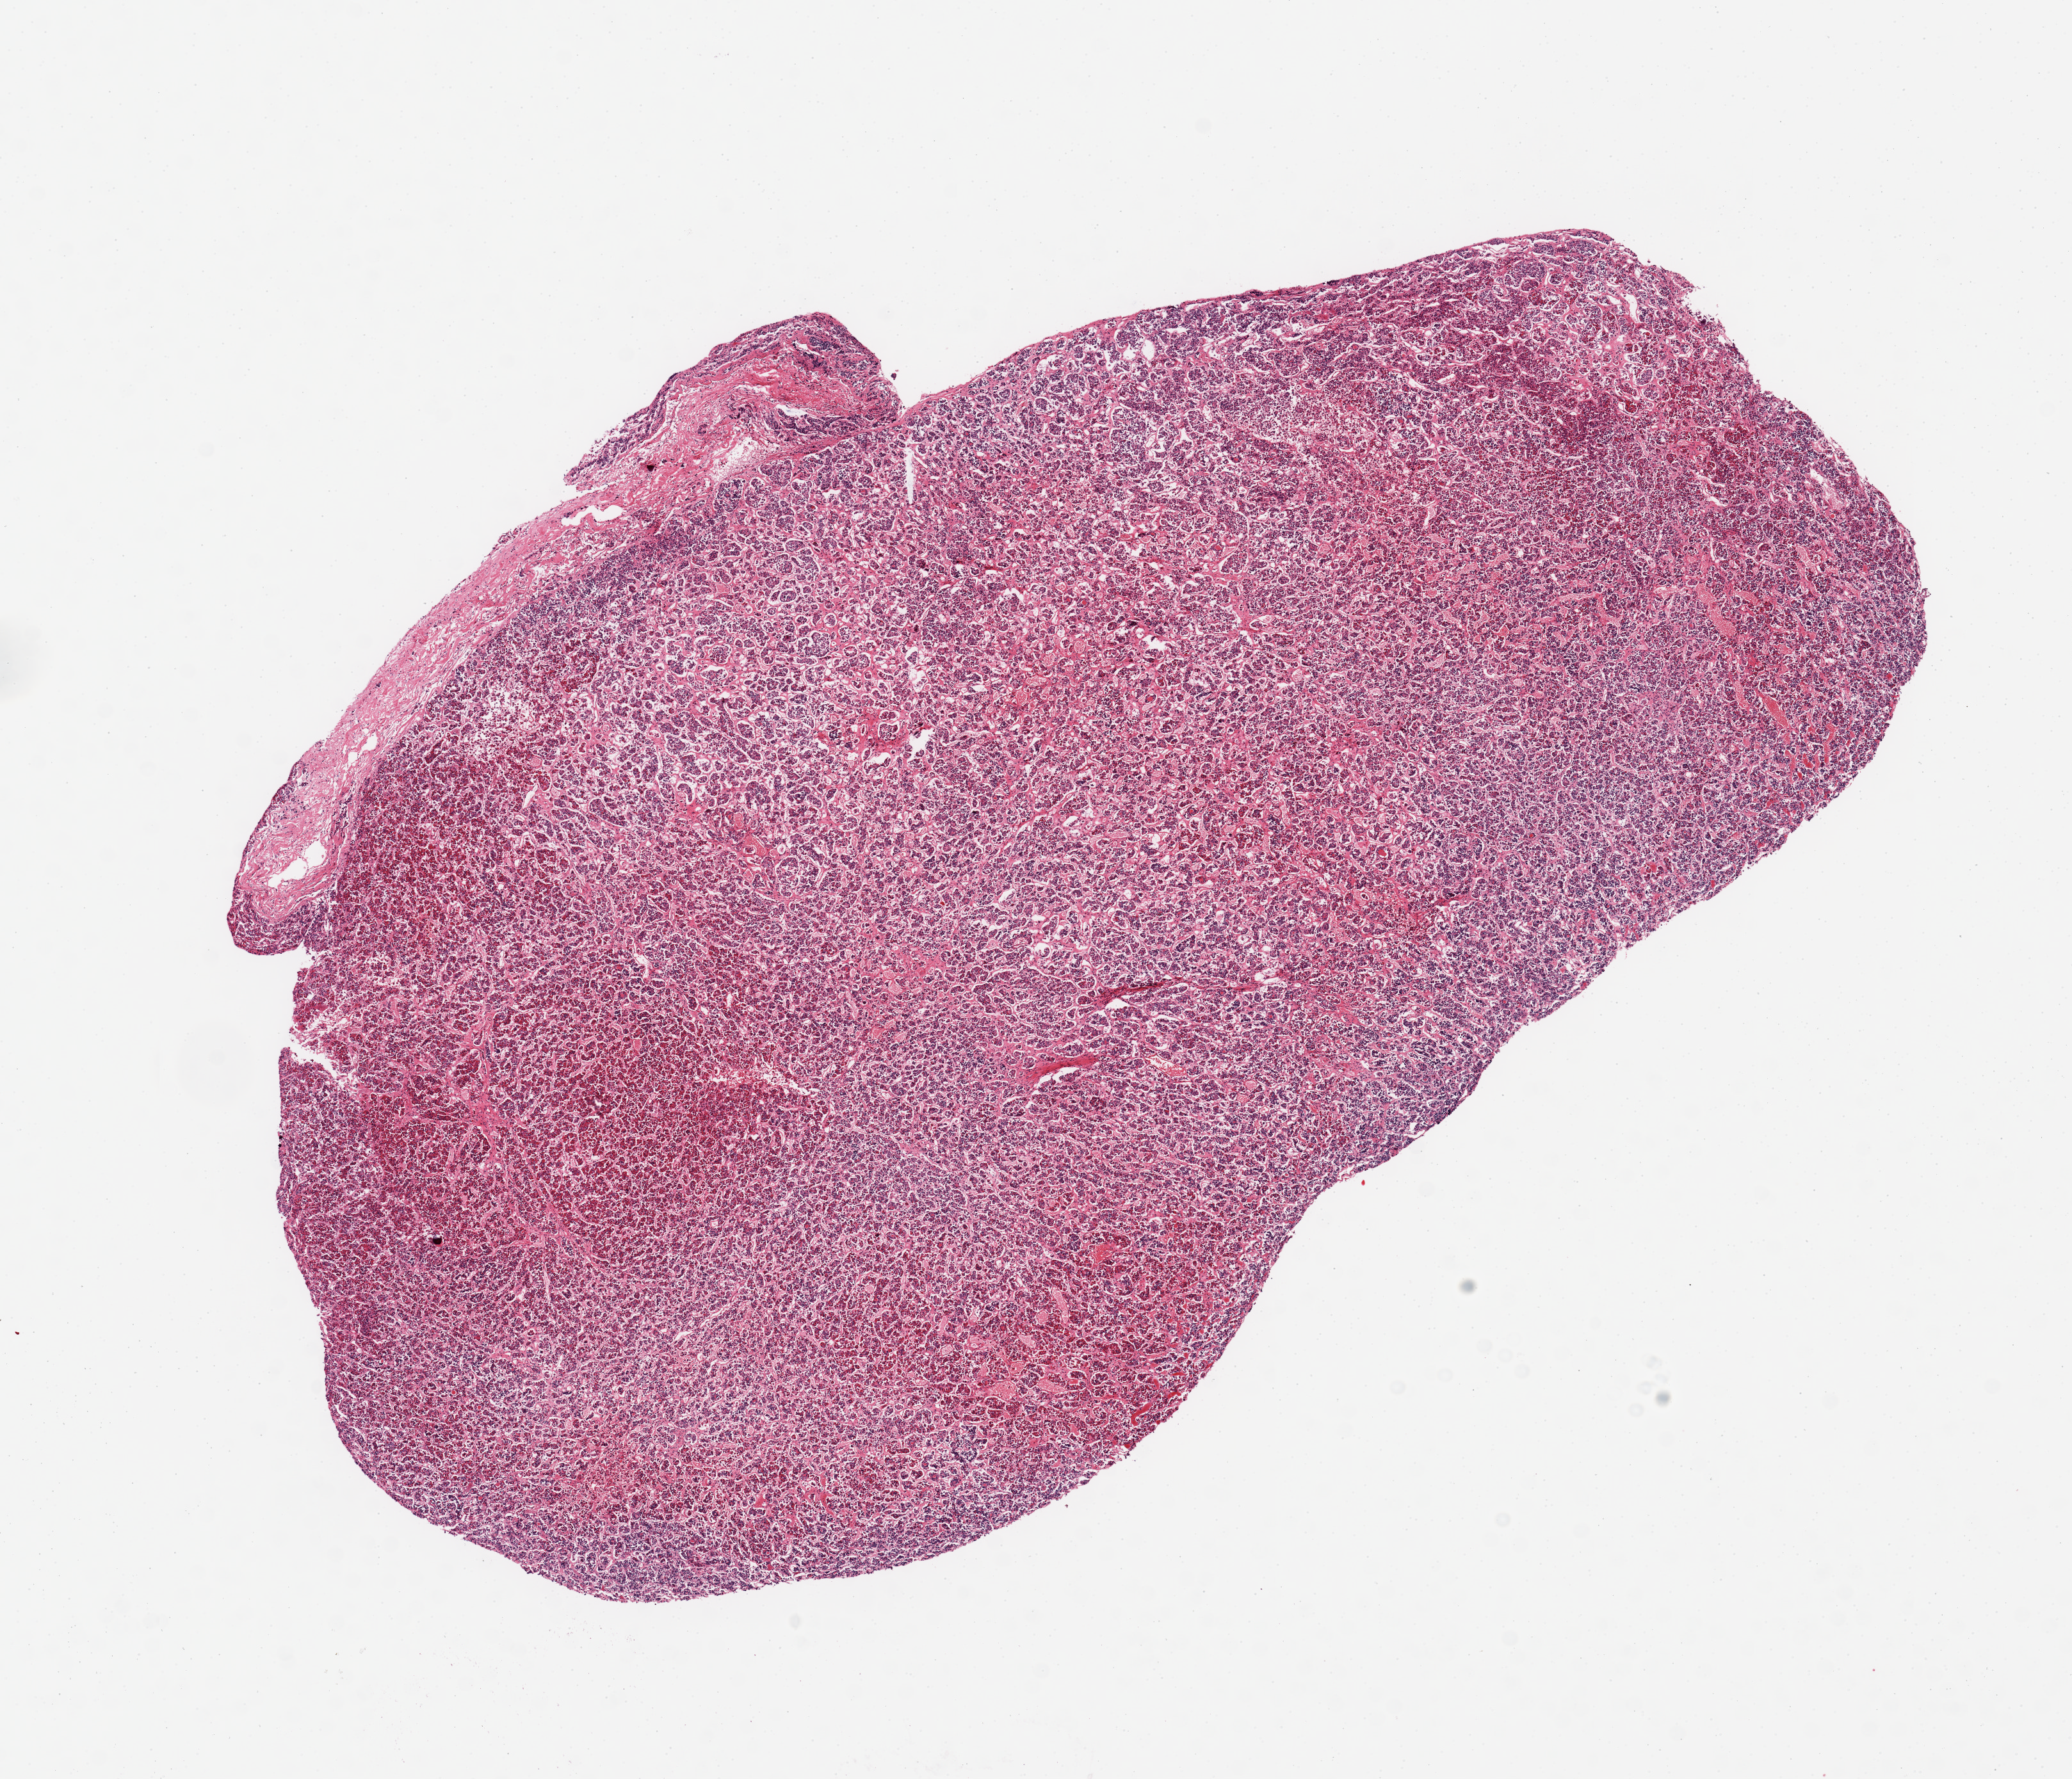
Whole-slide image, haematoxylin and eosin stain — shown as a low-resolution overview of the whole scanned area (about 12.8 x 11.0 mm, from a 20x scan); PAXgene-fixed, paraffin-embedded tissue; sampled site (target tissue): pituitary; donor tissue sample. Donor sex: female.
Pathologist's review note for this sample: 1 piece; all anterior lobe.